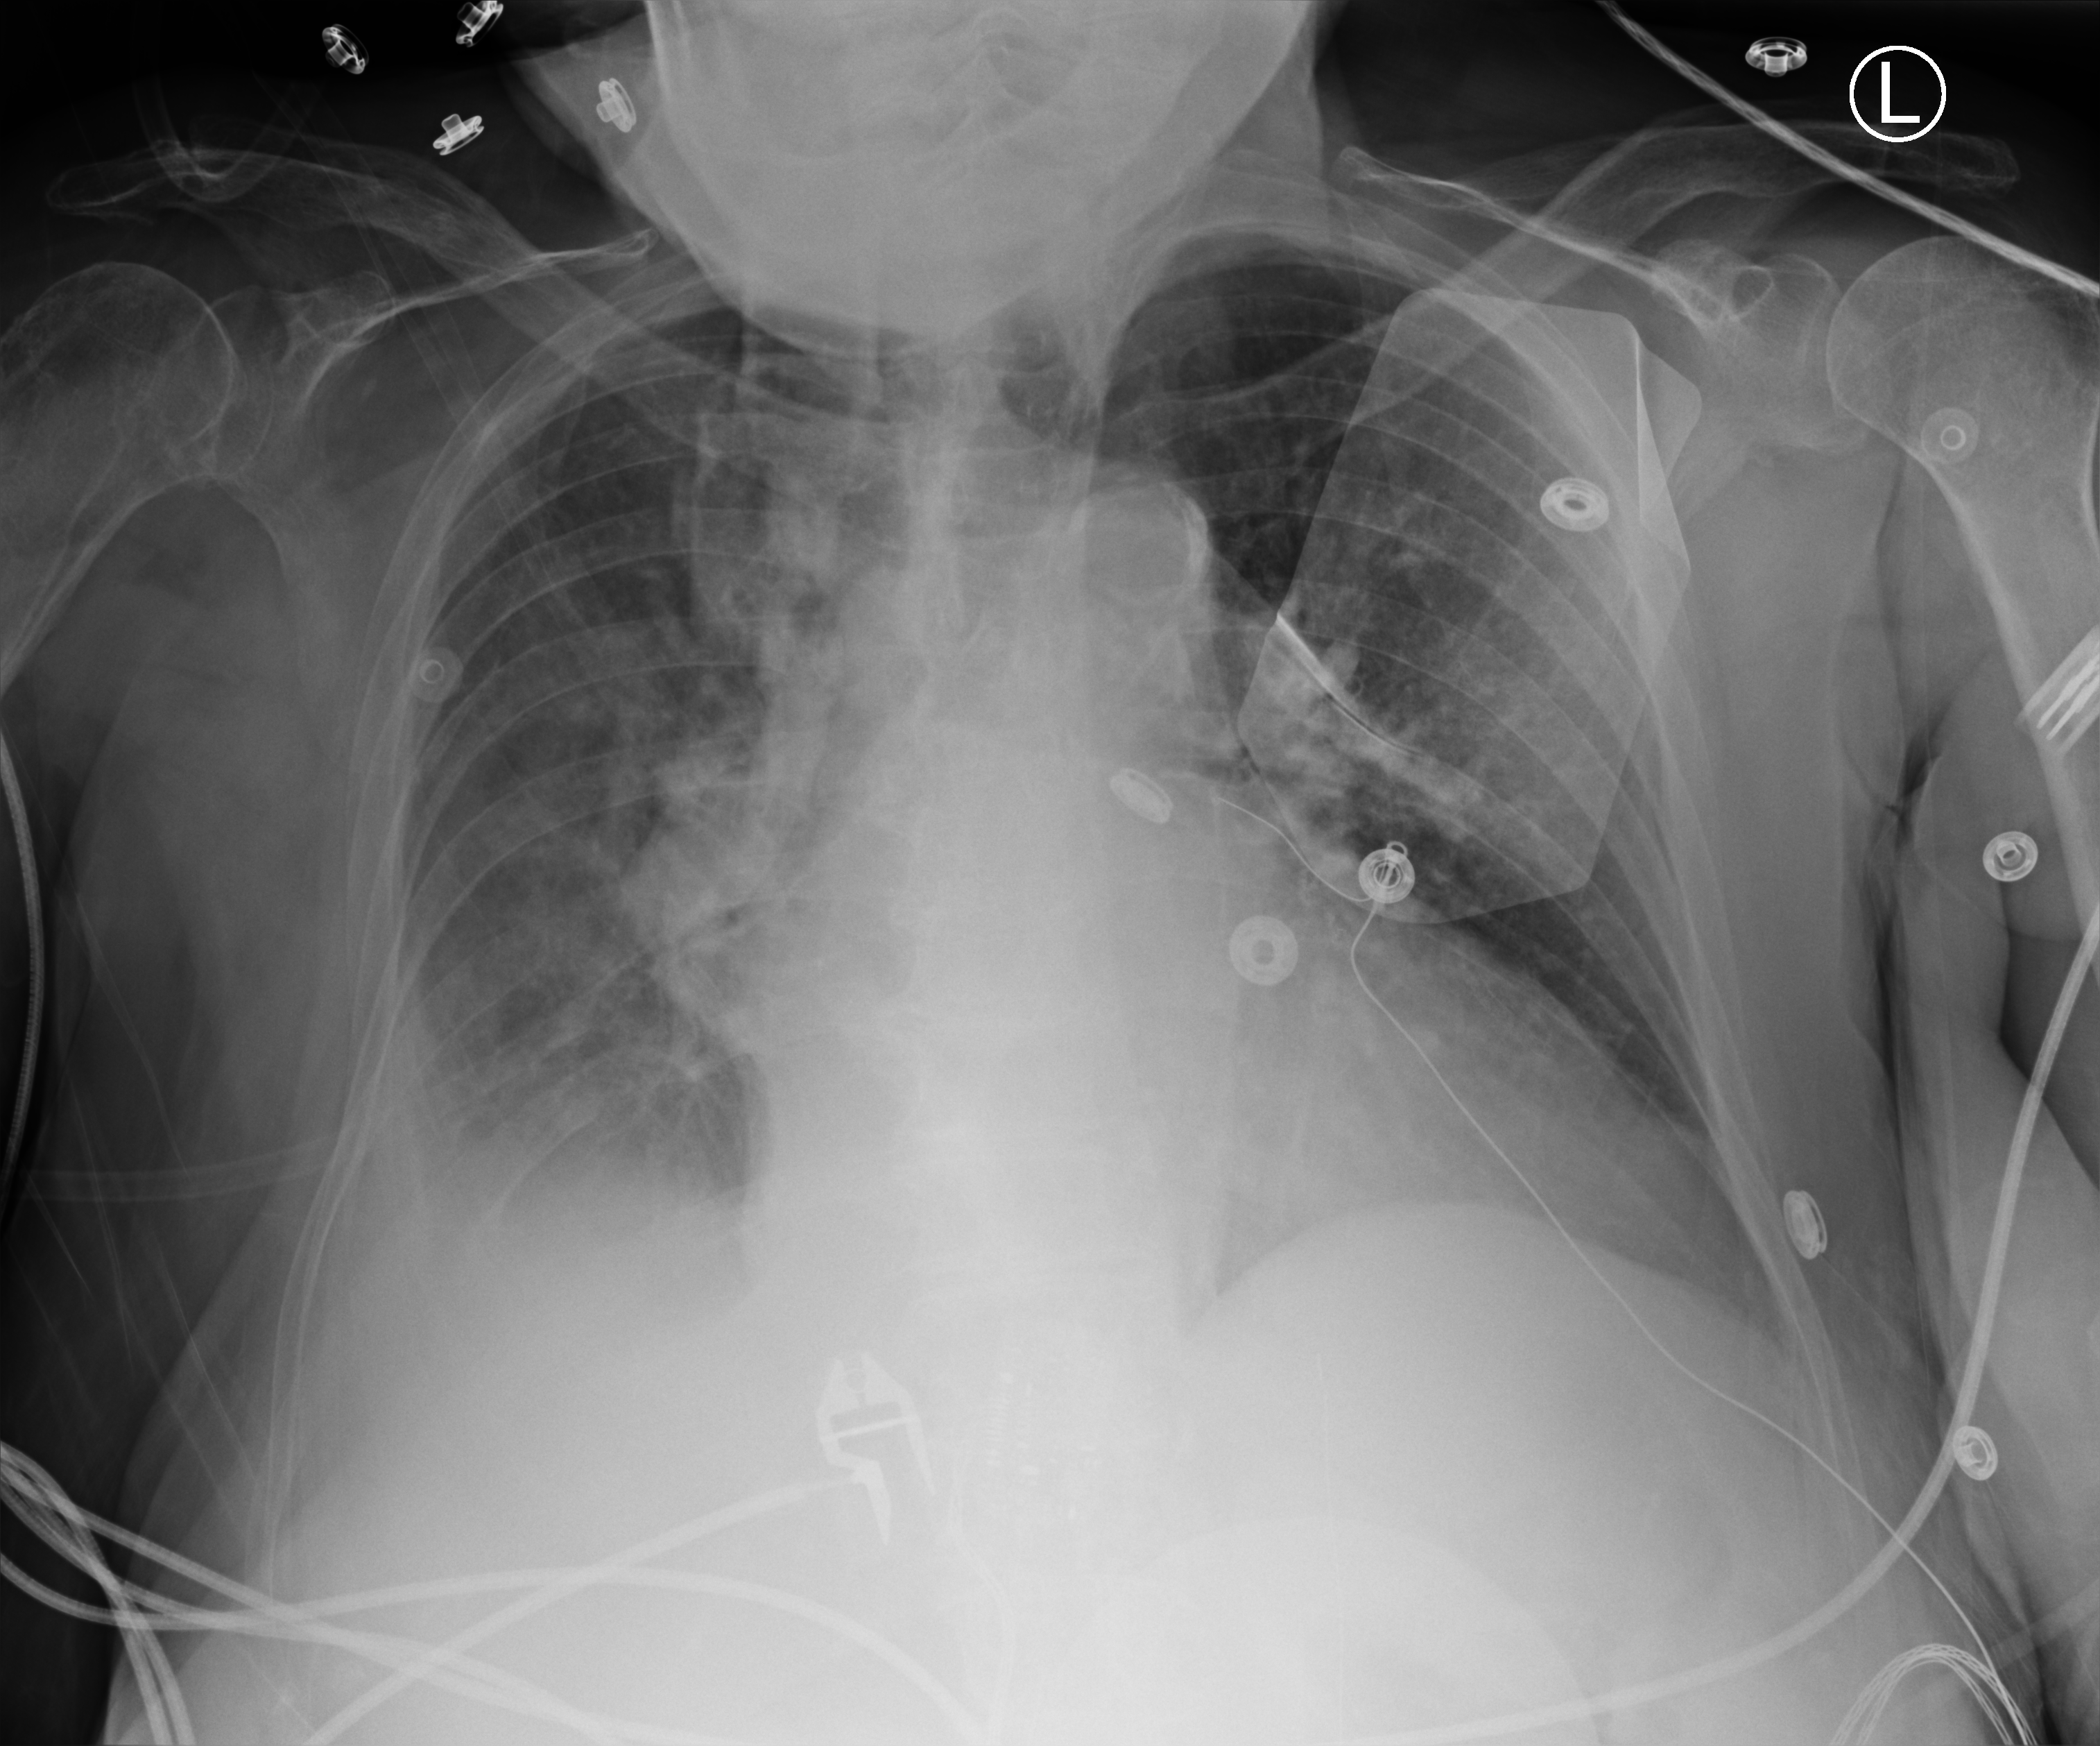
Portable chest radiograph; anteroposterior (AP) projection. Patient hospitalised with COVID-19; female, aged 75–90 years.
Admission-level facts for this patient (not findings on this image; timing relative to this image not recorded): other chronic lung disease (admission record): no.